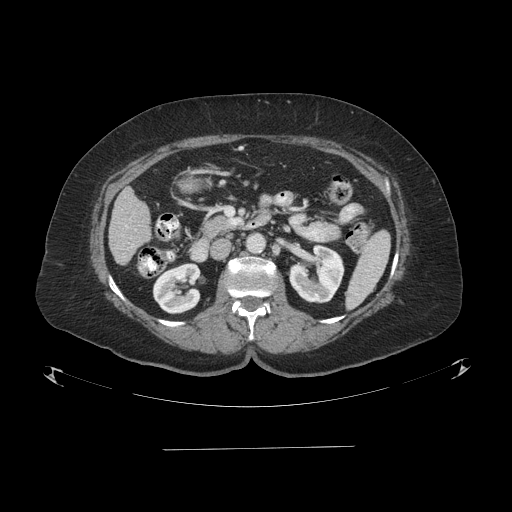
Contrast-enhanced abdominal CT (liver protocol), one axial slice; position 28 of 103 along the scan axis; reconstruction kernel STANDARD; one of 2 acquisitions stored at this slice position; soft-tissue window (W 400 / L 40 HU); 2.5 mm slice thickness; 512 × 512 image matrix. From the clinical record (not read from this slice): diagnosis: hepatocellular carcinoma (patient treated with transarterial chemoembolisation; whether this scan precedes or follows treatment is not stated here); TNM stage (as recorded): Stage-IIIA; Child-Pugh class: A; tumour size: 5.2 cm.
Outlined on this slice (semi-automatically segmented with operator editing):
- liver parenchyma outside the tumour (the mass and vessels are separate outlines, so this box may not span the whole liver): box from (x=108, y=188) to (x=150, y=264) px